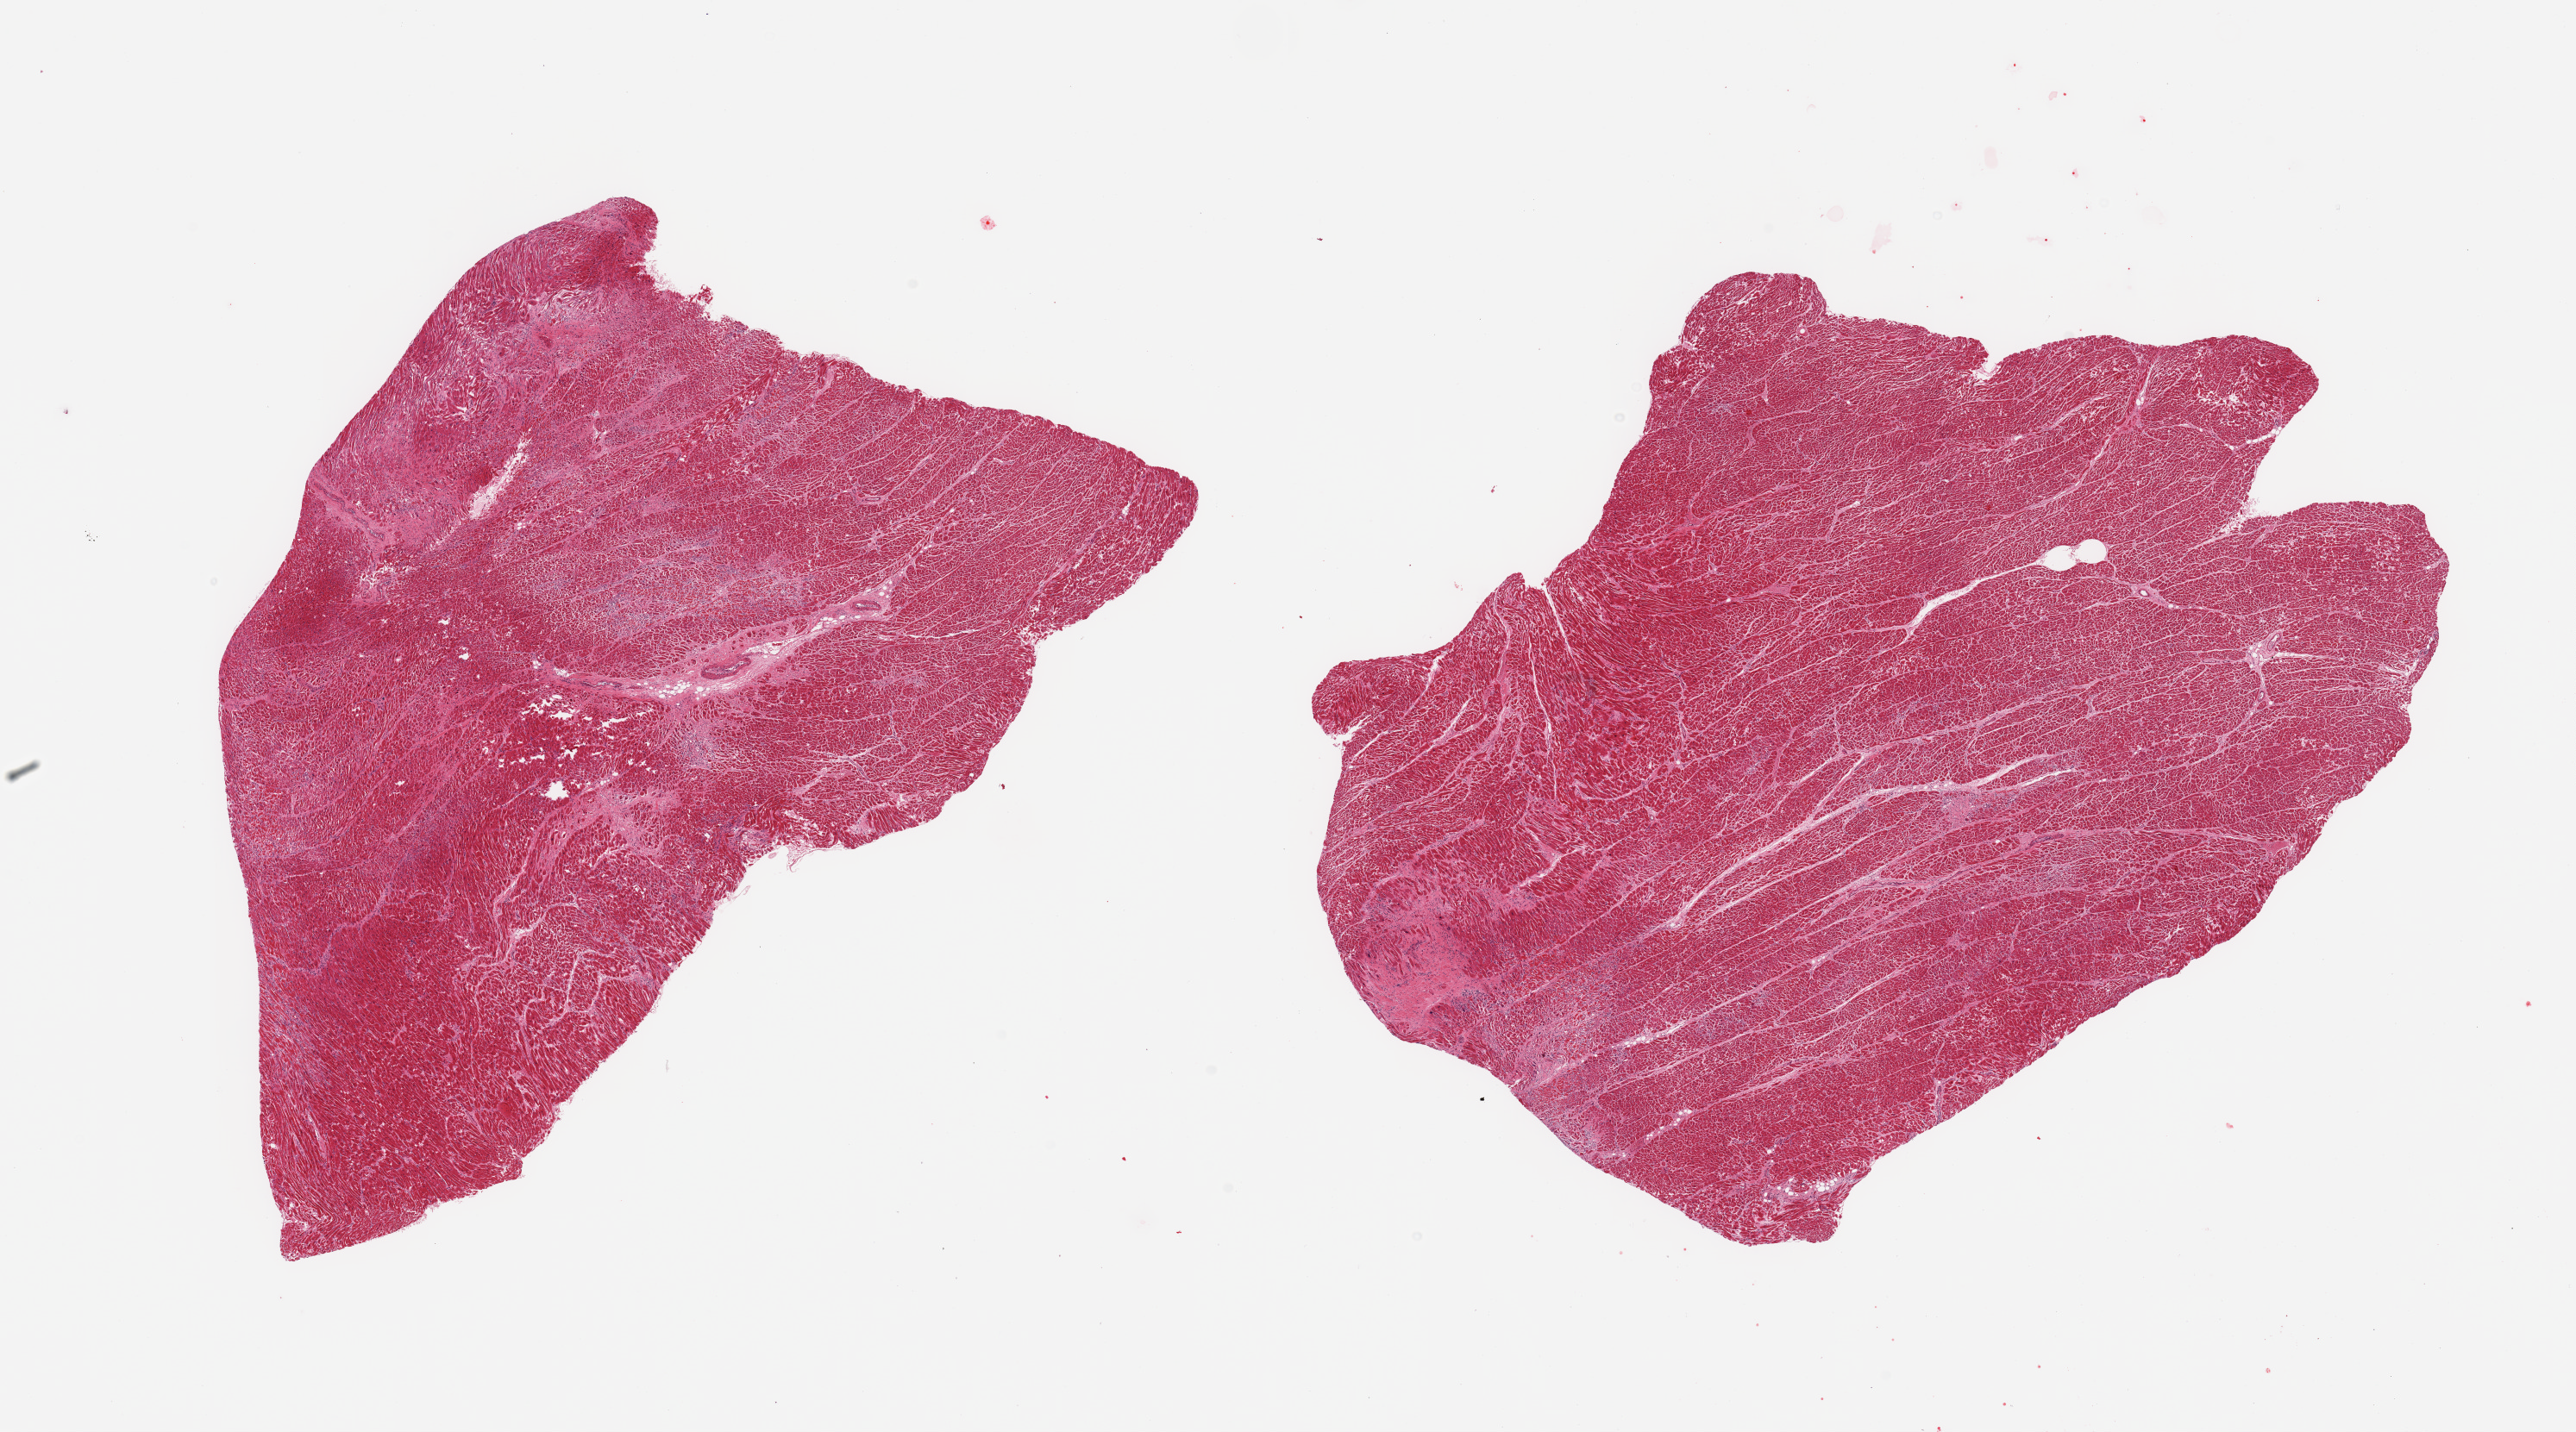
Digitized hematoxylin and eosin (H&E)-stained section, whole scanned area (about 23.6 x 13.1 mm, slide scanned at 20x) shown as a low-resolution overview; PAXgene-fixed, paraffin-embedded tissue; section of heart (target tissue); donor tissue sample. Donor sex: male.
Review note (as recorded): 2 pieces; patchy fibrosis (old infarct) and hypereosinophilia (very recent ischemia).